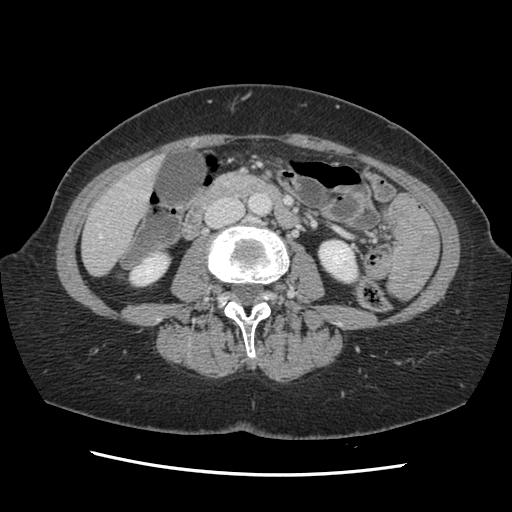
Contrast-enhanced abdominal CT, one axial slice; position 37 of 141 along the scan axis; 120 kVp; soft-tissue window (W 400 / L 40 HU); 2.5 mm slice thickness; 512 × 512 image matrix. Female patient, age 61 years. Case-level facts recorded for this patient, not image findings: diagnosis: colorectal cancer liver metastases, imaged before liver resection; multiple liver metastases: no; largest metastasis: 2.4 cm; disease in both lobes: no.
Annotated regions visible in this slice (outlined manually by an expert reader):
- hepatic veins: box from (x=97, y=168) to (x=149, y=238) px
- liver: (x=84, y=159)–(x=160, y=275)
- planned liver remnant (the part of the liver to remain after resection): (x=84, y=164)–(x=159, y=275)